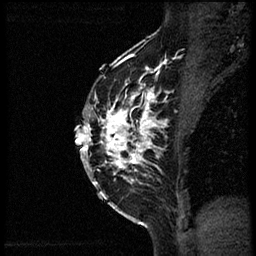
Breast MRI (dynamic contrast-enhanced), one sagittal slice. Slice 38 of 56 in the series (ordered by position). Dynamic contrast-enhanced study with each time point stored as its own series, time point 2 of 3 at this slice position (early post-contrast, ordered by acquisition time). 1.5 T. TE 4.2 ms, TR 21.3 ms. 2 mm slice thickness. 256 × 256 image matrix, field of view 200 × 200 mm. Patient: female, 41 years. Case-level facts recorded for this patient, not image findings: setting: breast cancer imaged before/during neoadjuvant chemotherapy; receptor status: HER2-positive.
Structures marked on this image (semi-automatically segmented with operator editing):
- analysis volume of interest (the breast-tissue region the enhancement analysis was run in; not a lesion): box from (x=85, y=73) to (x=177, y=205) px
- tumour enhancement mask (voxels above the 100 % enhancement threshold inside the analysis volume of interest): (x=85, y=76)–(x=169, y=185)